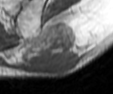
MRI of an extremity soft-tissue mass, one axial slice. Slice 18 of 42 in the series (ordered by position). MR volume resampled by the dataset authors to the PET/CT grid (not the native acquisition matrix). 3.27 mm slice thickness. 113 × 94 image matrix. Male patient. Case-level facts recorded for this patient, not image findings: histological type: leiomyosarcoma; grade: intermediate; site of the primary tumour: left pelvis.
Outlined on this slice (expert contour drawn on MRI and transferred to this co-registered scan by the dataset authors):
- gross tumour volume (mass): bounding box [x1, y1, x2, y2] px = [28, 23, 80, 74]